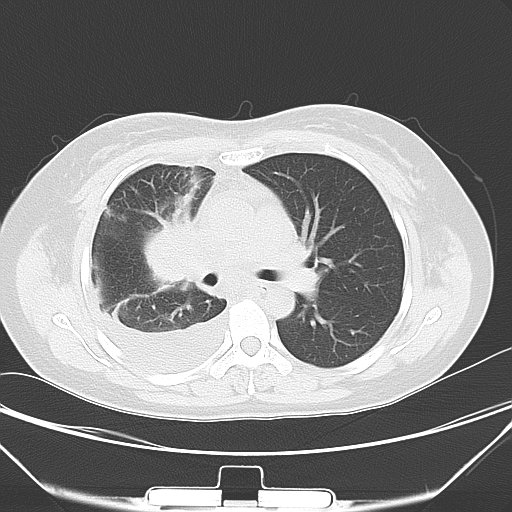
Chest CT, one axial slice; slice 32 of 52 in the series (ordered by position); 120 kVp; lung window (W 1500 / L -600 HU); 5 mm slice thickness; 512 × 512 image matrix, field of view 352 × 352 mm. Female patient, age 36 years. Case-level facts recorded for this patient, not image findings: clinical TNM (as recorded): T1b N2 M0; histopathological grade: G3.
Structures marked on this image (rectangle marked by the reading radiologist):
- lung tumour (recorded histology: adenocarcinoma): bounding box (x1, y1, x2, y2) in pixels: (138, 208, 206, 286)